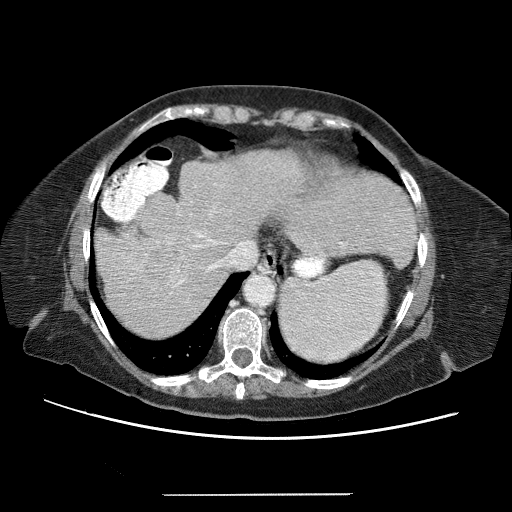
Contrast-enhanced abdominal CT (liver protocol), one axial slice. Position 50 of 65 along the scan axis. Soft-tissue window (W 400 / L 40 HU). 512 × 512 image matrix. From the clinical record (not read from this slice): diagnosis: hepatocellular carcinoma (patient treated with transarterial chemoembolisation; whether this scan precedes or follows treatment is not stated here); TNM stage (as recorded): Stage-IIIB; Child-Pugh class: A; tumour differentiation: moderately differentiated; tumour nodularity: uninodular.
Structures marked on this image (semi-automatic segmentation, software-assisted and operator-edited):
- liver parenchyma outside the tumour (the mass and vessels are separate outlines, so this box may not span the whole liver): box from (x=94, y=154) to (x=298, y=332) px
- mass: (x=123, y=236)–(x=187, y=313)
- liver vessels: (x=112, y=166)–(x=284, y=303)